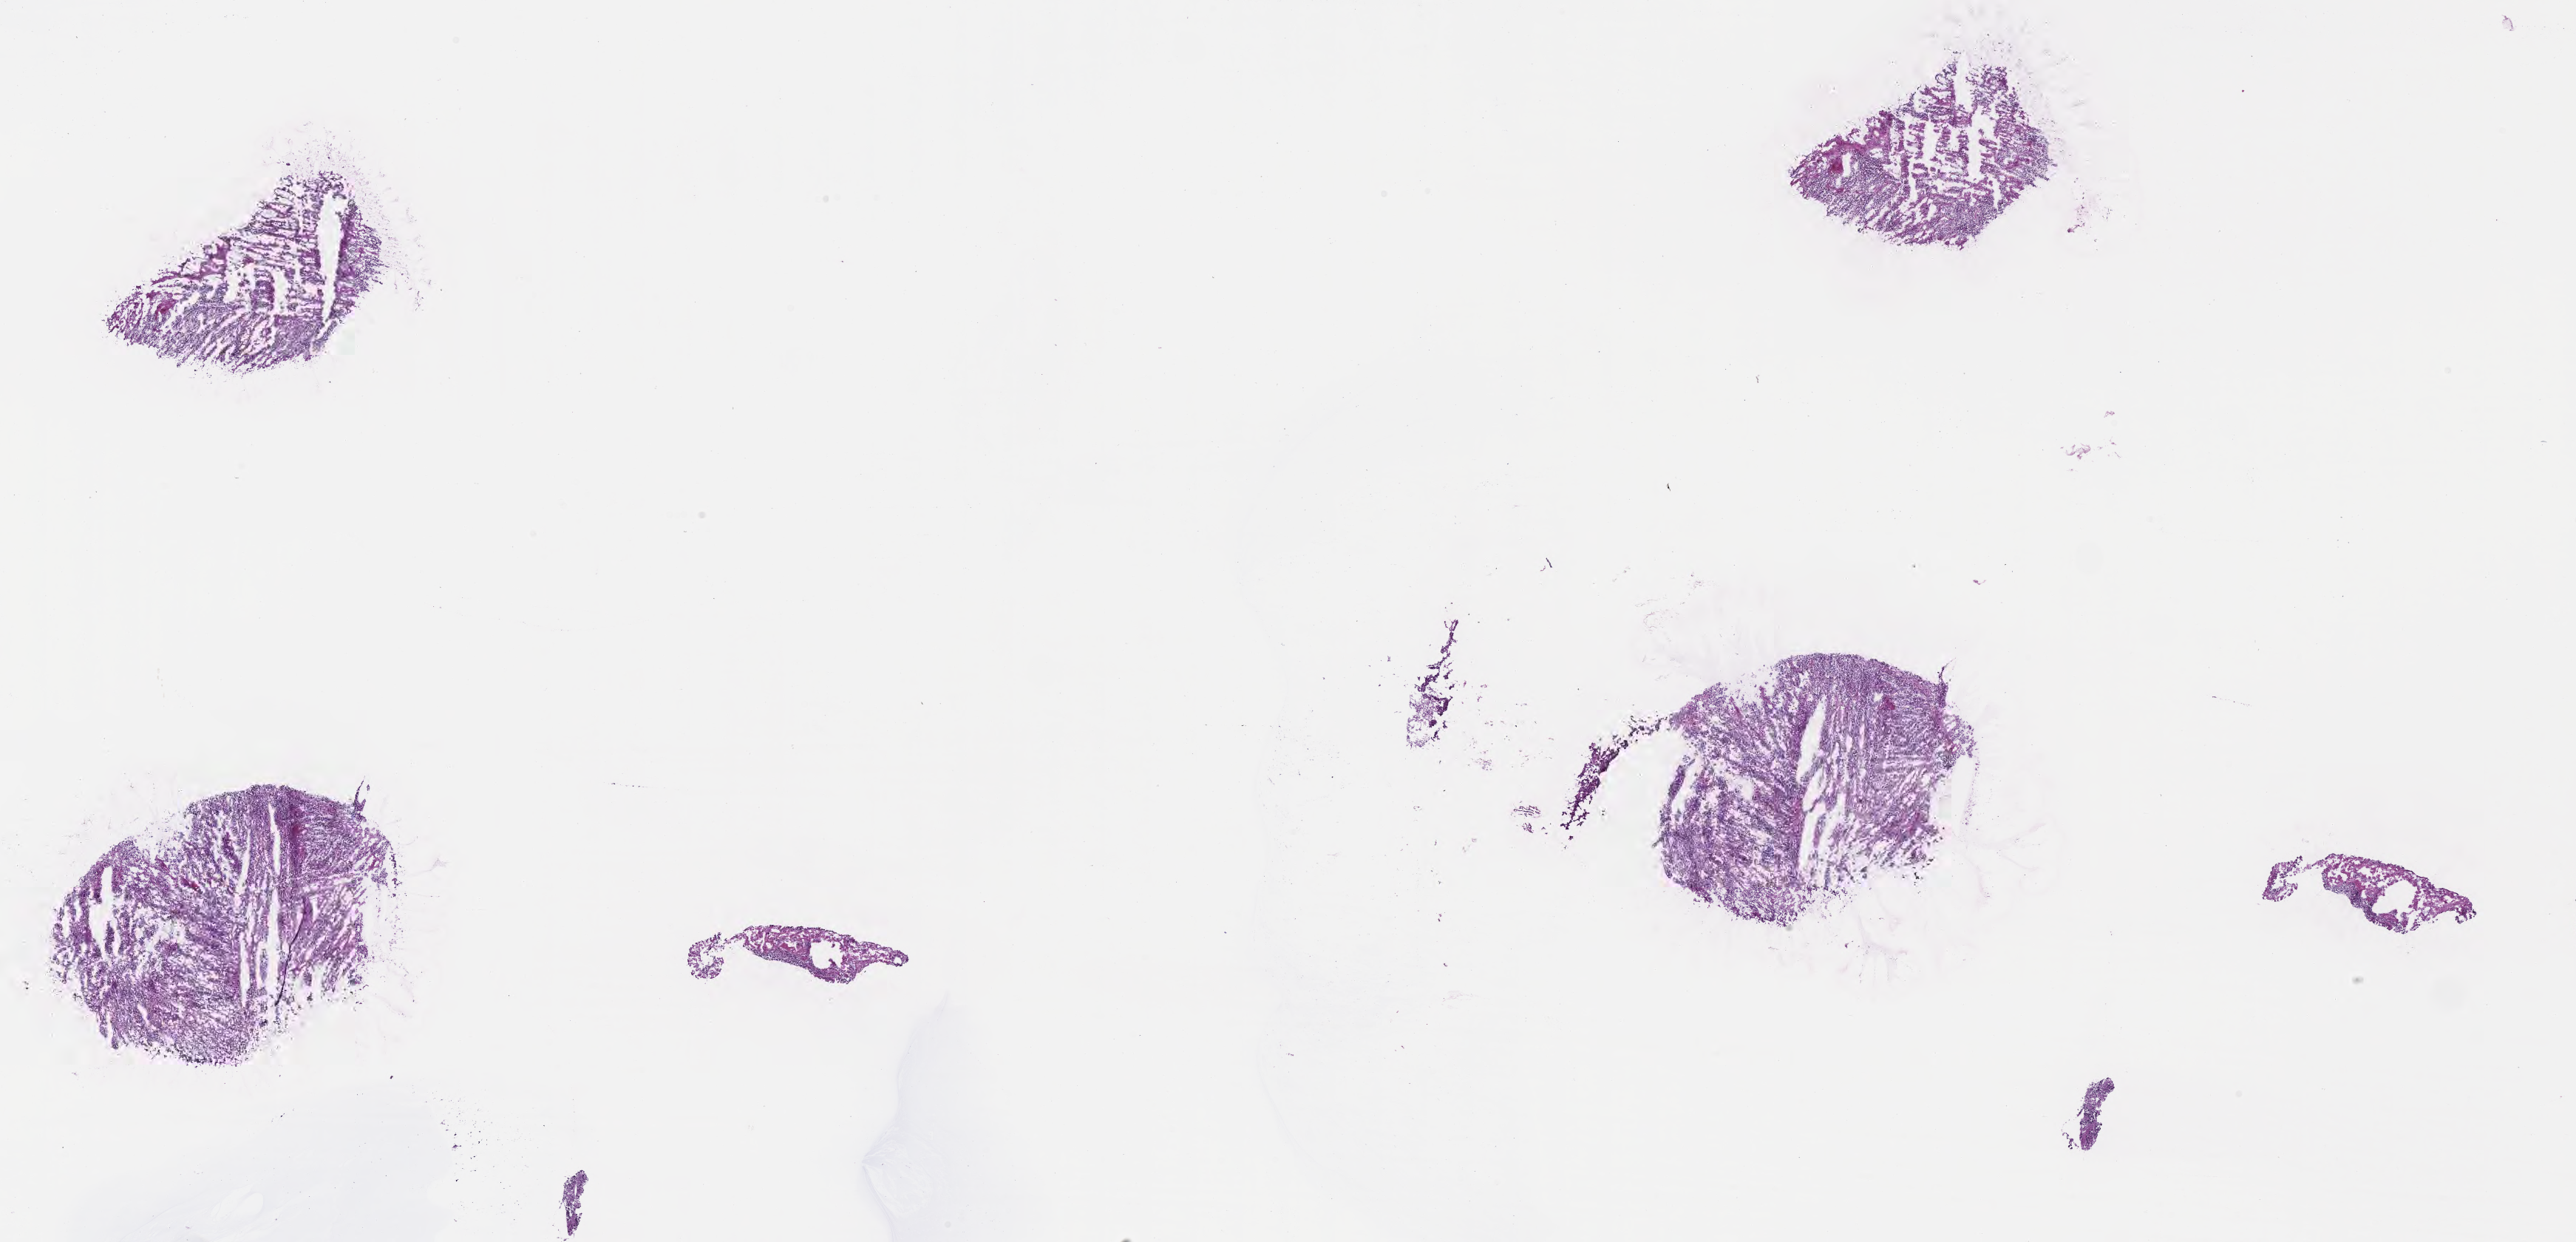
Whole-slide image, haematoxylin and eosin stain, low-resolution overview of the scanned area, about 28.2 x 13.6 mm; frozen section (tissue freezing medium); primary tumor; anatomic site: brain. Patient: female, age at initial diagnosis 11 years. Slide review estimates, as recorded: tumor cells 78%, tumor nuclei 88%, stromal cells 1%, necrosis 10%, normal cells 11%. Inflammatory infiltration, as recorded: lymphocyte infiltration 0%, monocyte infiltration 0%, neutrophil infiltration 0%.
Histologic diagnosis: Glioblastoma, NOS. Section: bottom of the tissue portion.